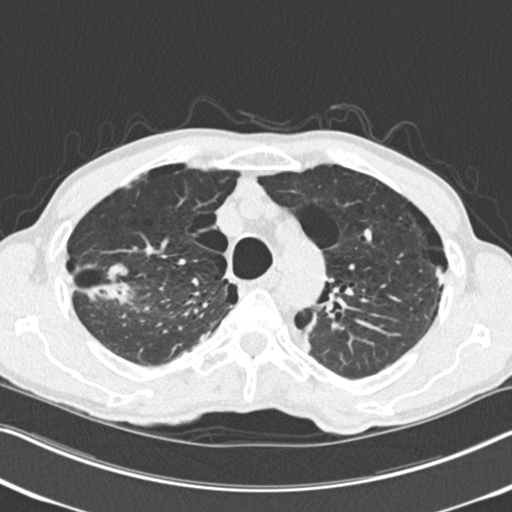
Low-dose screening chest CT, one axial slice. Slice 192 of 251 in the series (ordered by position). Reconstruction kernel B30f. 120 kVp. Lung window (W 1500 / L -600 HU). 2 mm slice thickness. 512 × 512 image matrix.
Outlined on this slice (manually delineated by an expert):
- lesion 1 (tumor, upper lobe of right lung): box from (x=87, y=264) to (x=134, y=303) px